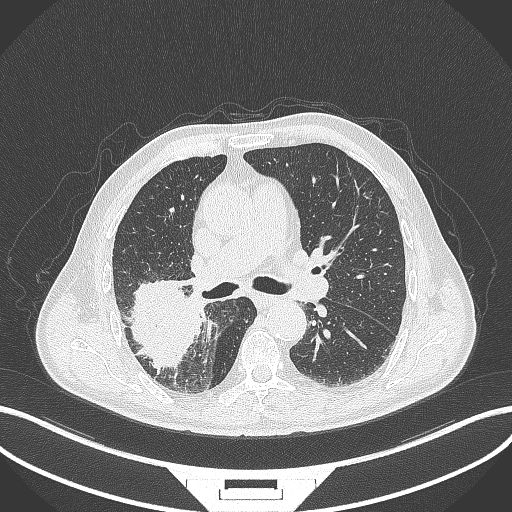
Chest CT, one axial slice; slice 245 of 429 in the series (ordered by position); reconstruction kernel B70f; lung window (W 1500 / L -600 HU); 1 mm slice thickness; 512 × 512 image matrix, field of view 400 × 400 mm. Male patient, age 72 years. From the clinical record (not read from this slice): clinical TNM (as recorded): T3 N2 M0.
Structures marked on this image (bounding box drawn by a radiologist):
- lung tumour (recorded histology: adenocarcinoma): box from (x=125, y=273) to (x=203, y=373) px